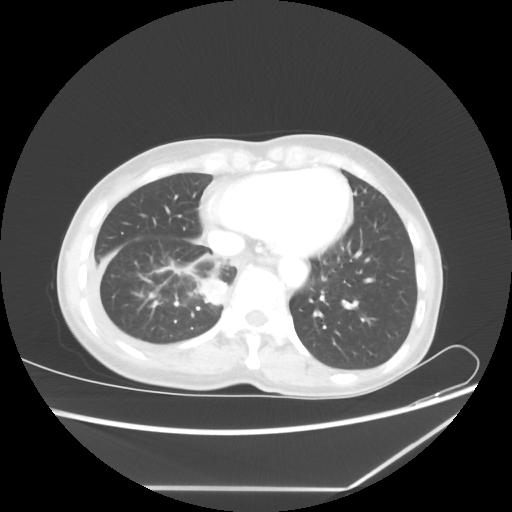
Chest CT, one axial slice; reconstruction kernel STANDARD; 80 kVp; lung window (W 1500 / L -600 HU); 512 × 512 image matrix. Patient: female, 59 years. From the clinical record (not read from this slice): clinical TNM (as recorded): T1c N1 M1.
Structures marked on this image (rectangle marked by the reading radiologist):
- lung tumour (recorded histology: adenocarcinoma): bounding box [x1, y1, x2, y2] px = [198, 276, 228, 307]